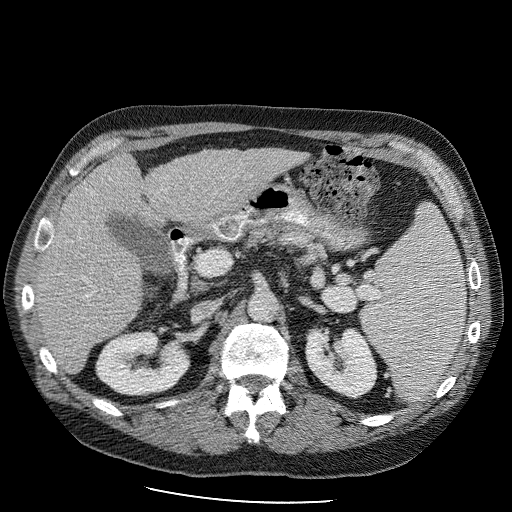
Contrast-enhanced abdominal CT (liver protocol), one axial slice; slice 47 of 98 in the series (ordered by position); reconstruction kernel STANDARD; soft-tissue window (W 400 / L 40 HU); 512 × 512 image matrix, field of view 400 × 400 mm. Case-level facts recorded for this patient, not image findings: diagnosis: hepatocellular carcinoma (patient treated with transarterial chemoembolisation; whether this scan precedes or follows treatment is not stated here); TNM stage (as recorded): Stage-II; Child-Pugh class: B; tumour differentiation: moderately differentiated.
Annotated regions visible in this slice (semi-automatic segmentation, software-assisted and operator-edited):
- liver parenchyma outside the tumour (the mass and vessels are separate outlines, so this box may not span the whole liver): box from (x=35, y=148) to (x=308, y=370) px
- liver vessels: (x=49, y=242)–(x=91, y=301)